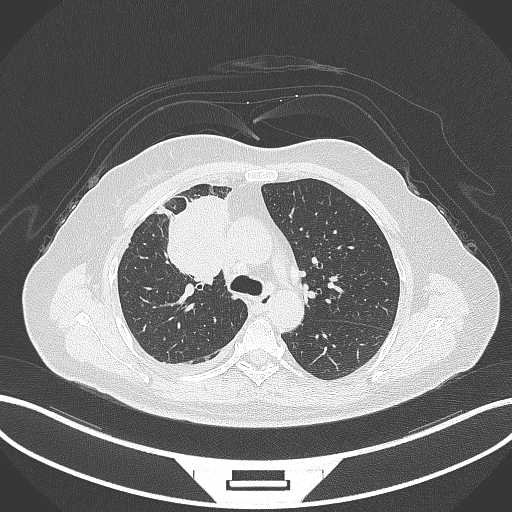
Chest CT, one axial slice; slice 191 of 305 in the series (ordered by position); reconstruction kernel B70f; 120 kVp; lung window (W 1500 / L -600 HU); 1 mm slice thickness; 512 × 512 image matrix. Patient: female, 52 years. From the clinical record (not read from this slice): clinical TNM (as recorded): T3 N1 M1.
Annotated regions visible in this slice (rectangle marked by the reading radiologist):
- lung tumour (recorded histology: adenocarcinoma): bounding box <167,195,234,284> (left, top, right, bottom; pixels)